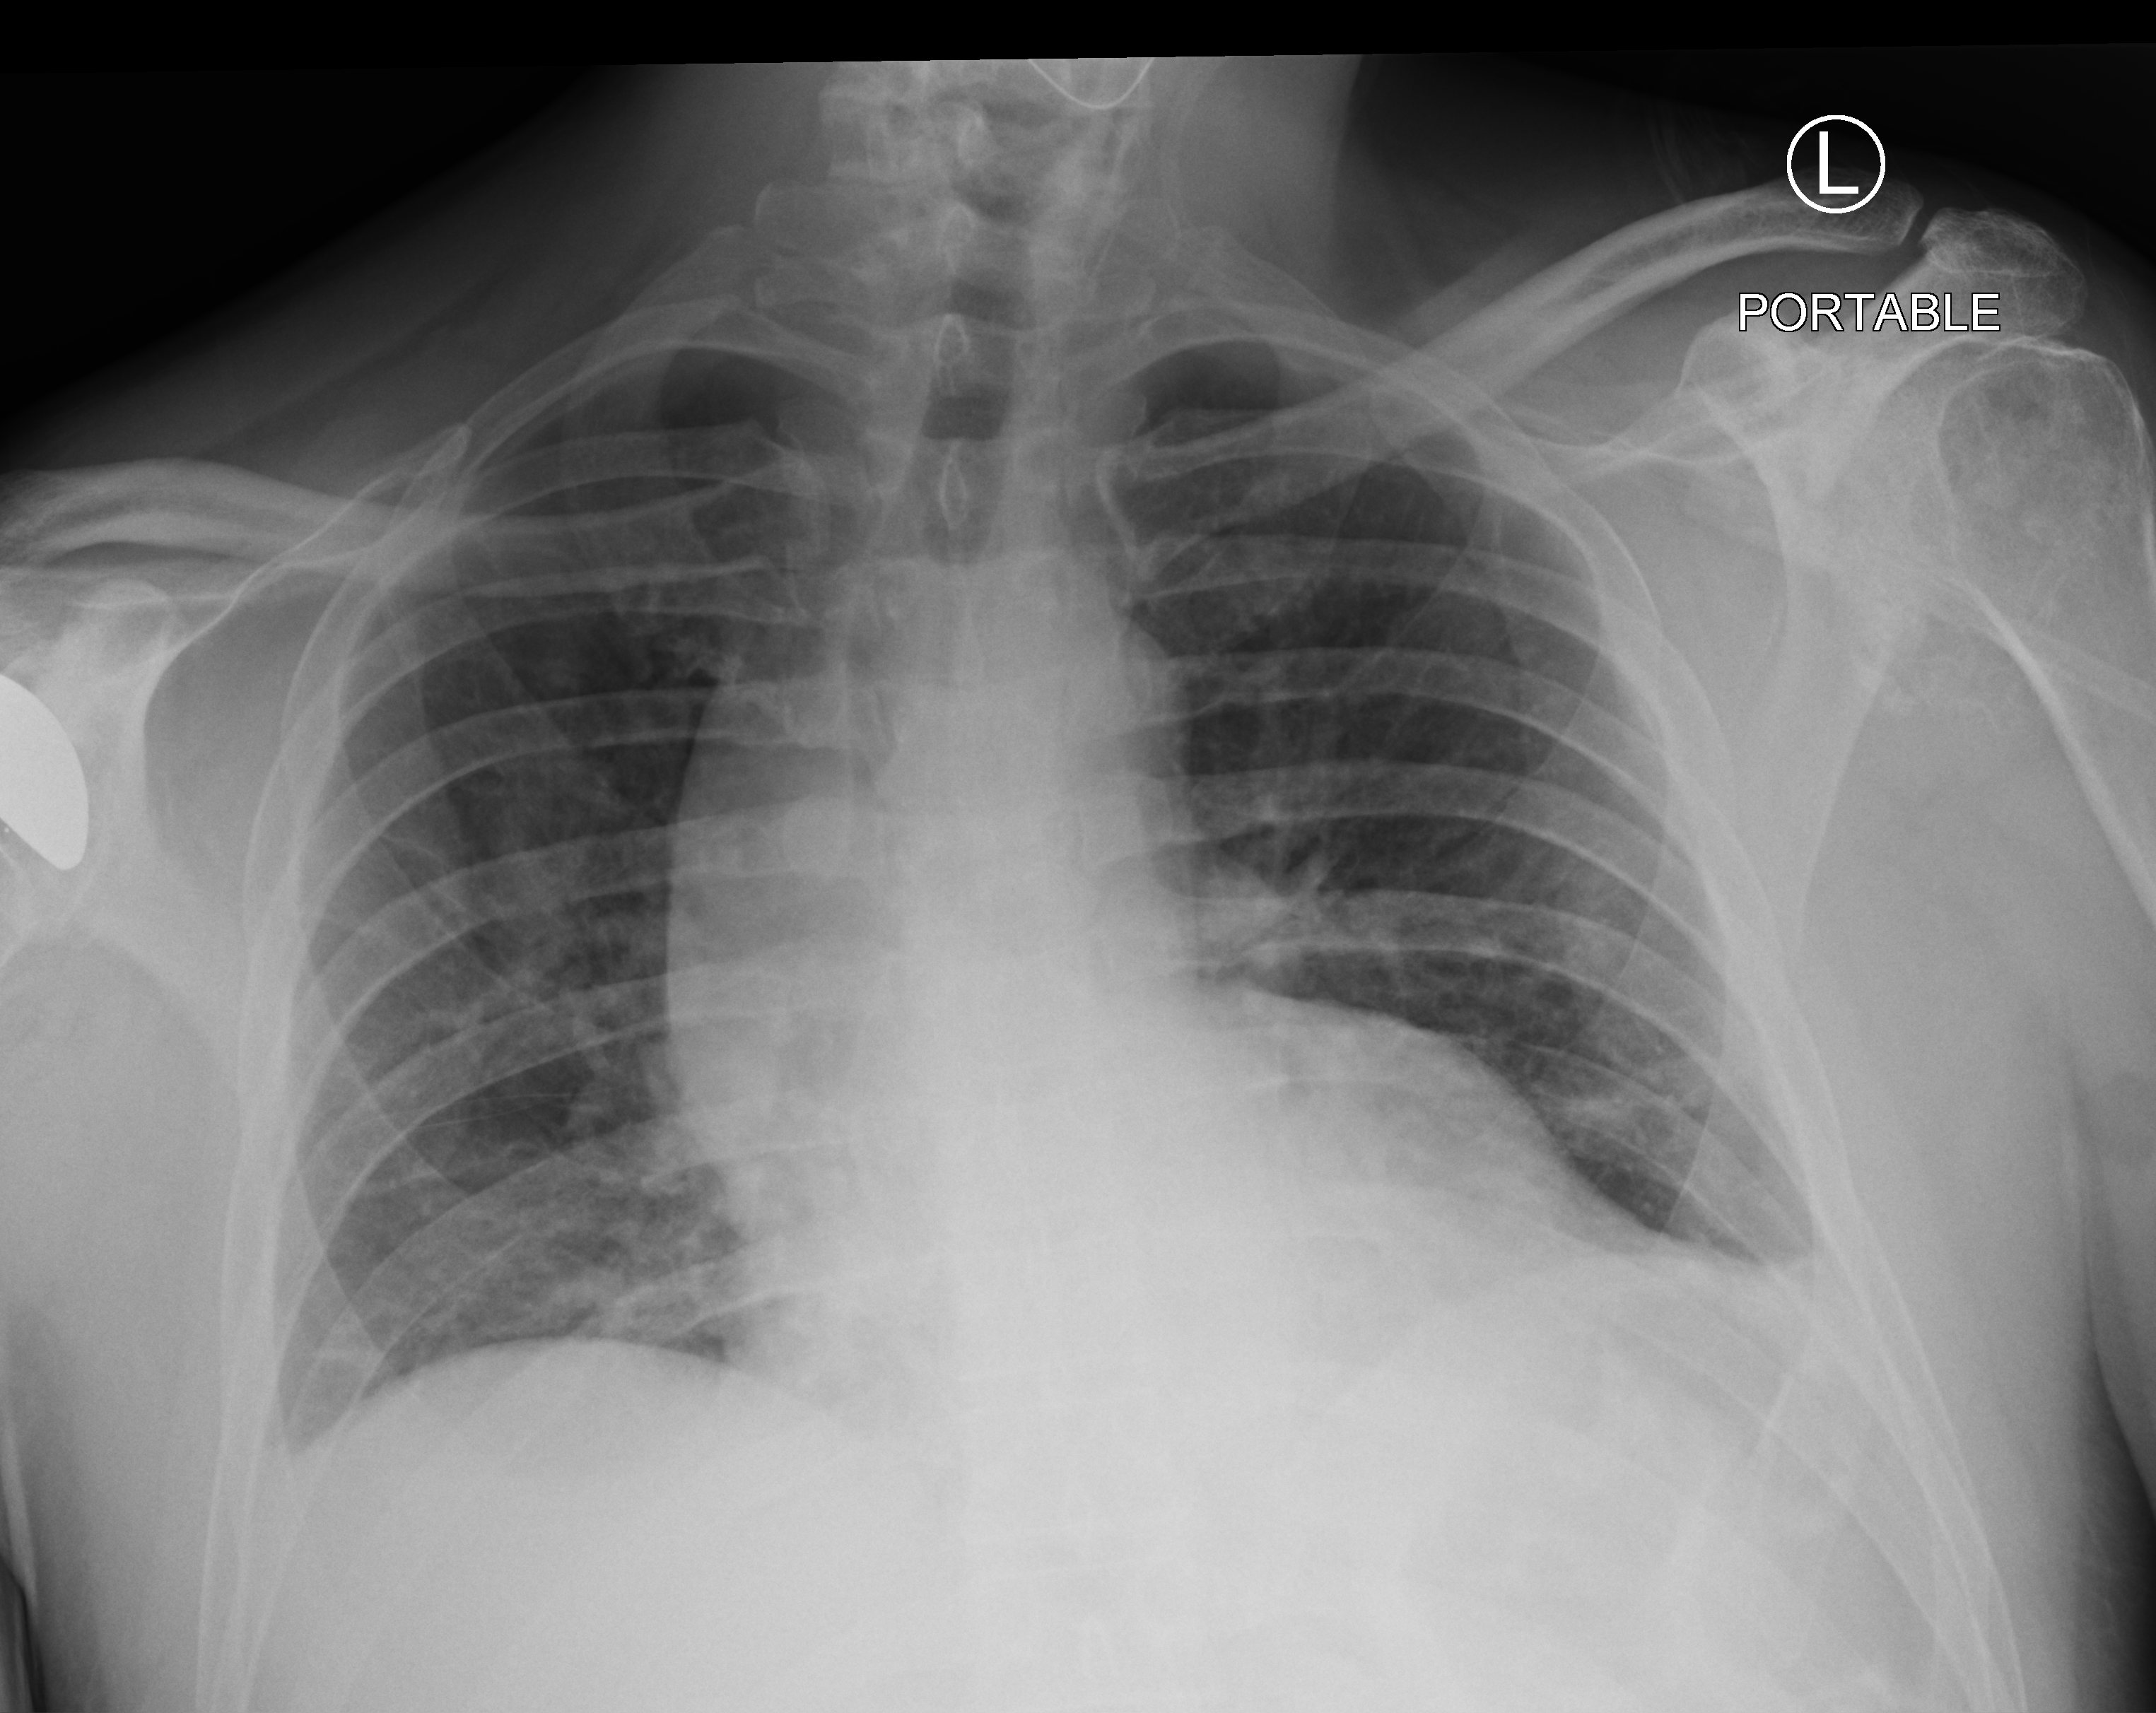
Portable chest radiograph; anteroposterior (AP) projection. Patient hospitalised with COVID-19; male, aged 60–74 years.
From the hospital-stay record, not from the radiograph (when in the stay this image was taken is not recorded): hypertension (admission record): no.